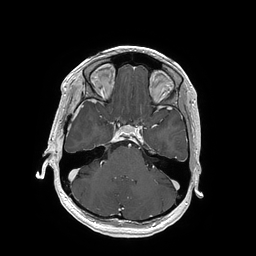
Brain MRI from a brain-tumour surgery series, one axial slice; position 120 of 202 along the scan axis; T1-weighted post-contrast; 1 mm slice thickness; 256 × 256 image matrix, field of view 250 × 250 mm. Case-level facts recorded for this patient, not image findings: histopathology: Glioblastoma; WHO grade: 4; IDH mutation: no.
Structures marked on this image (manually delineated by an expert):
- tumour: bounding box [x1, y1, x2, y2] px = [89, 118, 91, 120]